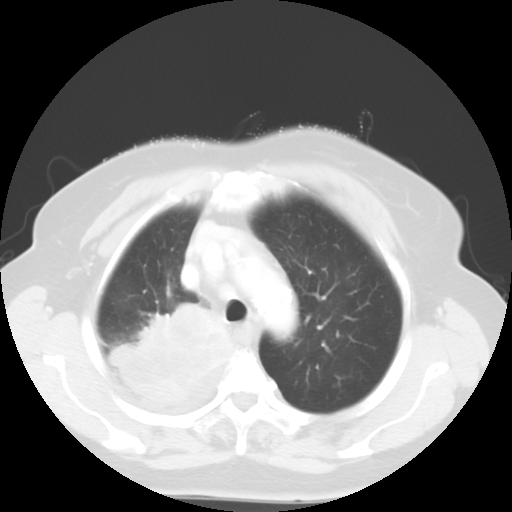
Chest CT, one axial slice. Position 42 of 52 along the scan axis. Reconstruction kernel STANDARD. Lung window (W 1500 / L -600 HU). 5 mm slice thickness. 512 × 512 image matrix, field of view 333 × 333 mm. Patient: female, 81 years. From the clinical record (not read from this slice): clinical TNM (as recorded): T4 N3 M1b.
Annotated regions visible in this slice (rectangle marked by the reading radiologist):
- lung tumour (recorded histology: adenocarcinoma): bounding box [x1, y1, x2, y2] px = [104, 298, 228, 410]